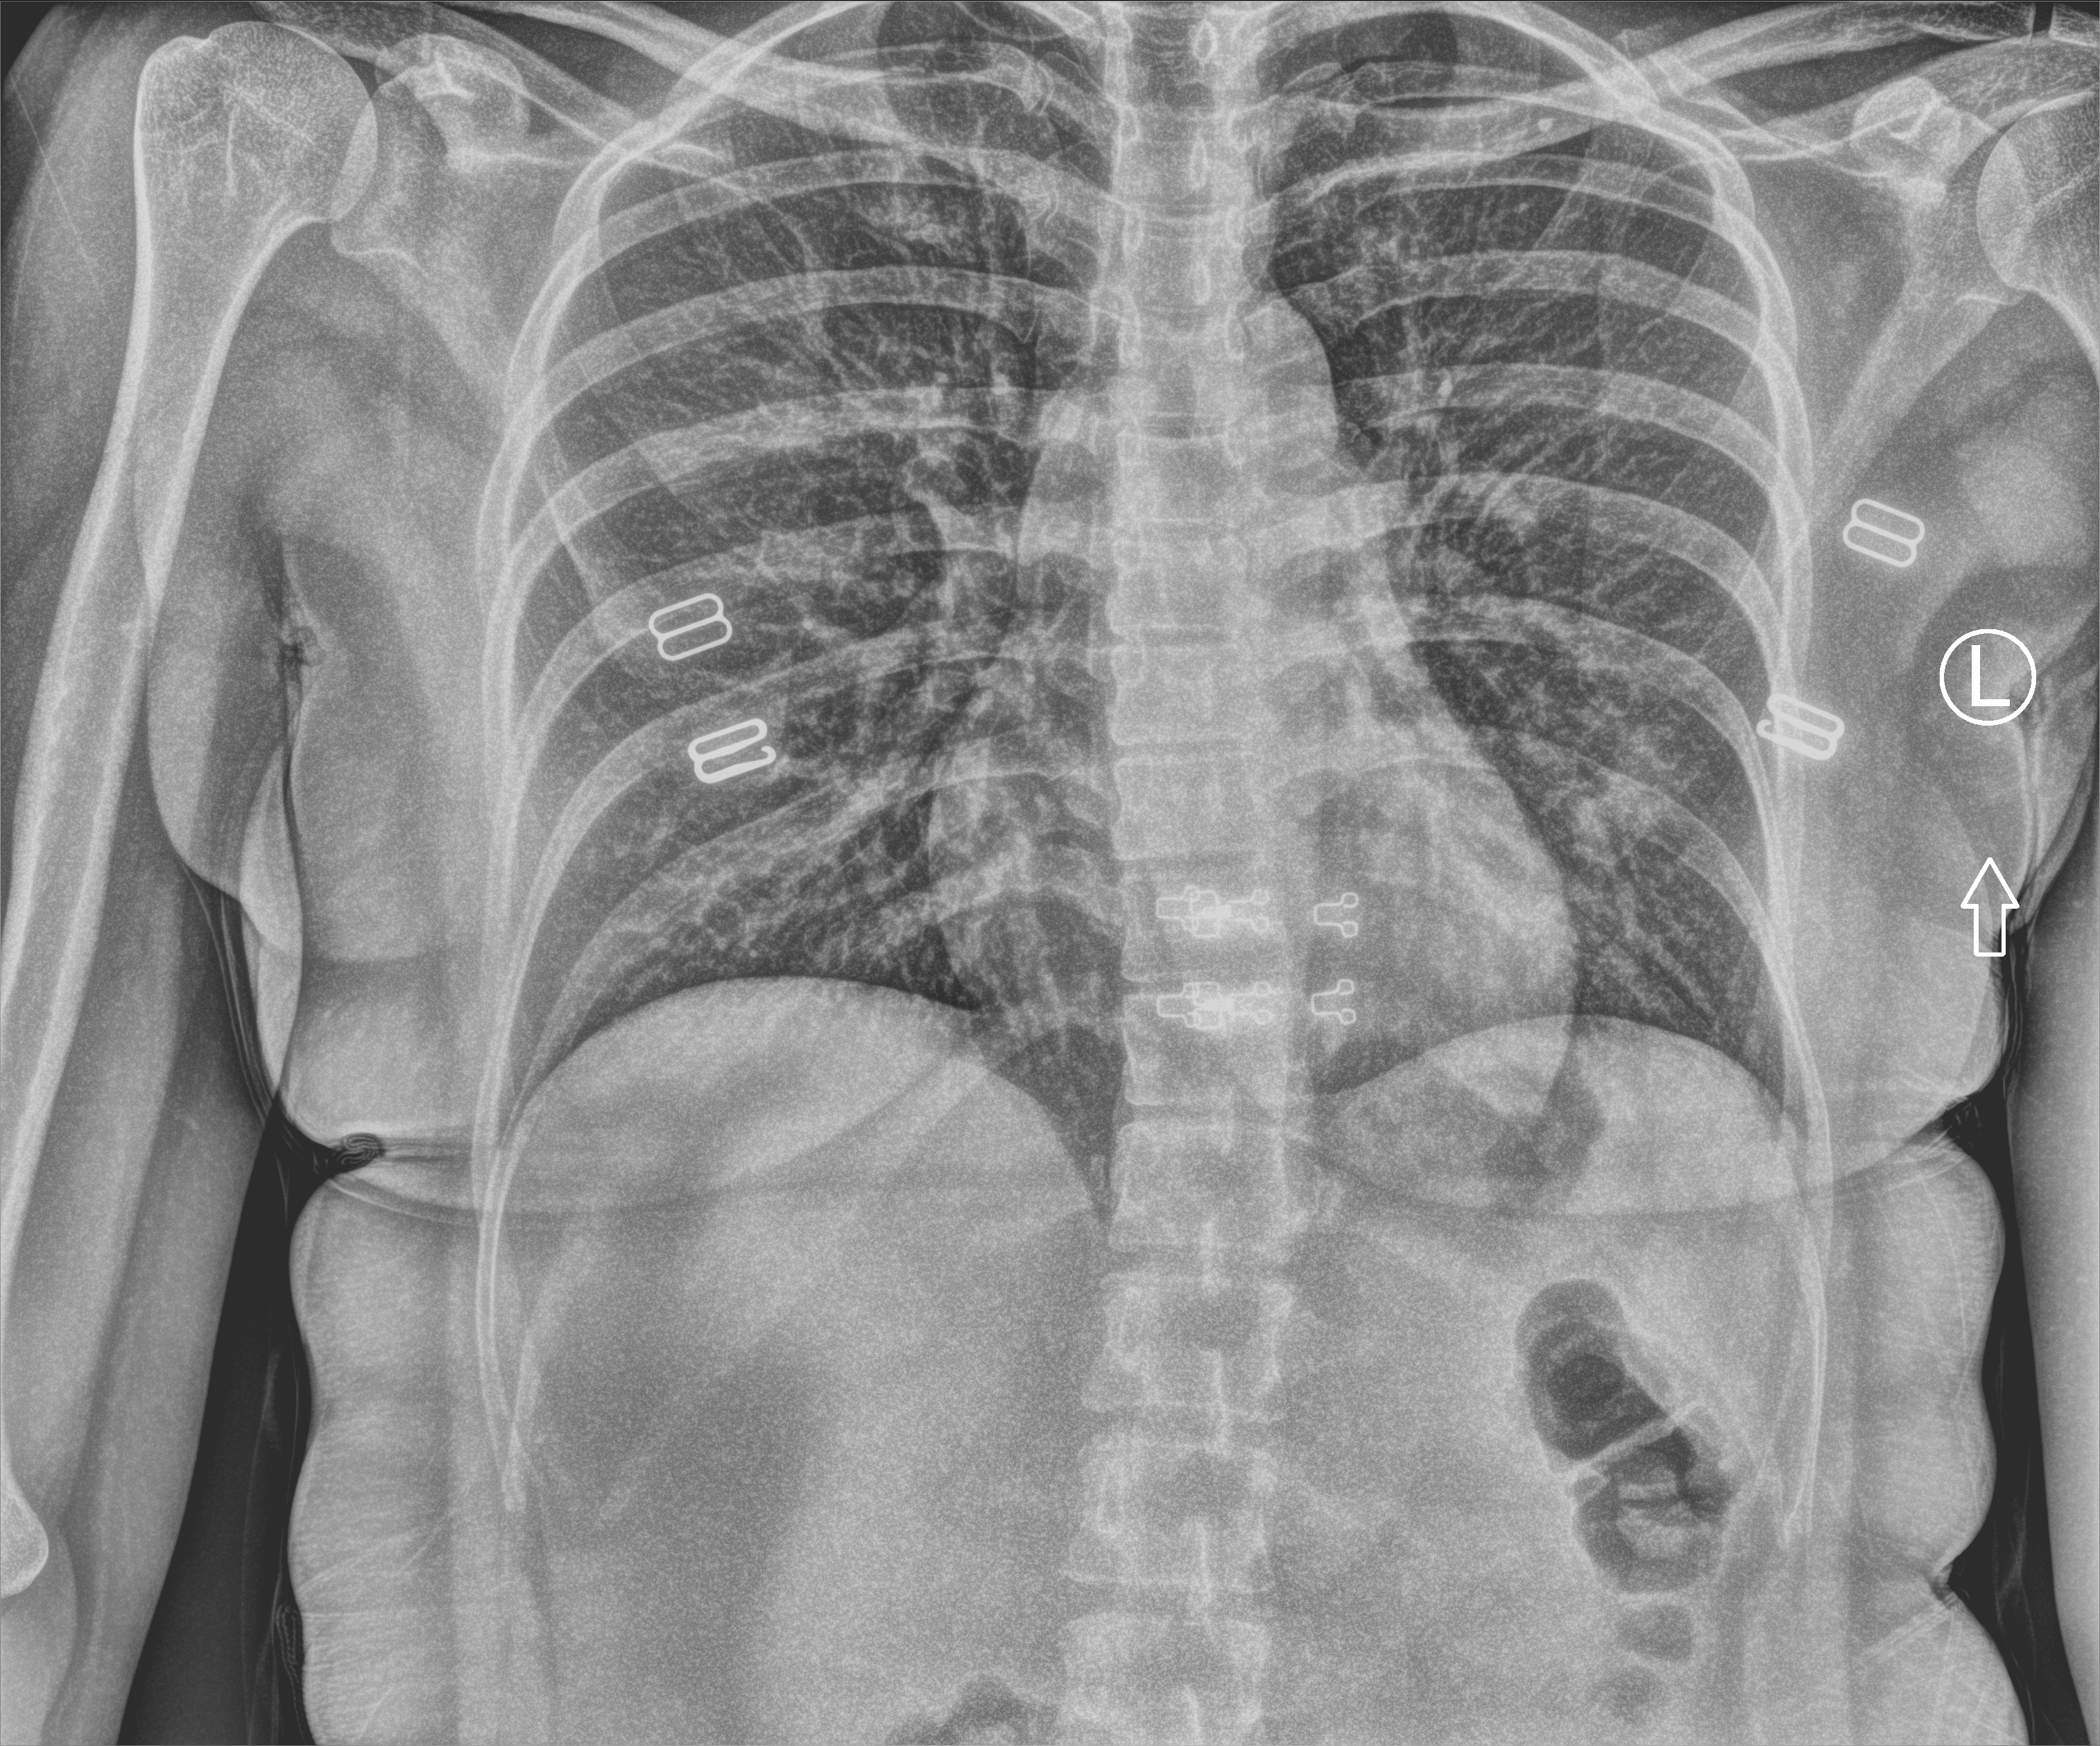
Chest X-ray (portable), anteroposterior (AP) projection. Female patient hospitalised with COVID-19, age 18–59 years.
From the hospital-stay record, not from the radiograph (when in the stay this image was taken is not recorded): mechanically ventilated during this hospital stay: no.